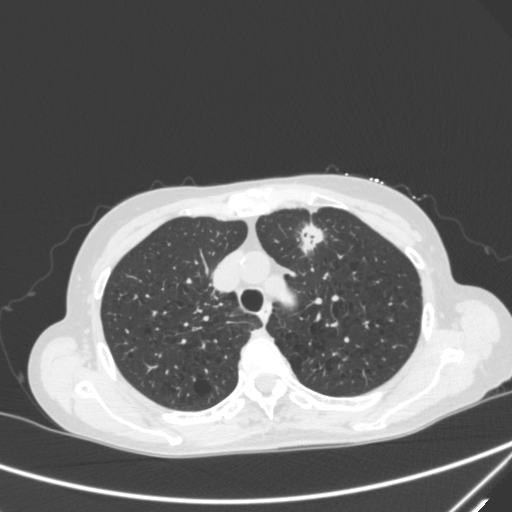
Chest CT, one axial slice. Slice 230 of 300 in the series (ordered by position). Lung window (W 1500 / L -600 HU). 512 × 512 image matrix. Patient: female, 71 years. From the clinical record (not read from this slice): clinical TNM (as recorded): T1c N0 M0; histopathological grade: G2-3.
Outlined on this slice (bounding box drawn by a radiologist):
- lung tumour (recorded histology: adenocarcinoma): bounding box (x1, y1, x2, y2) in pixels: (293, 220, 333, 265)